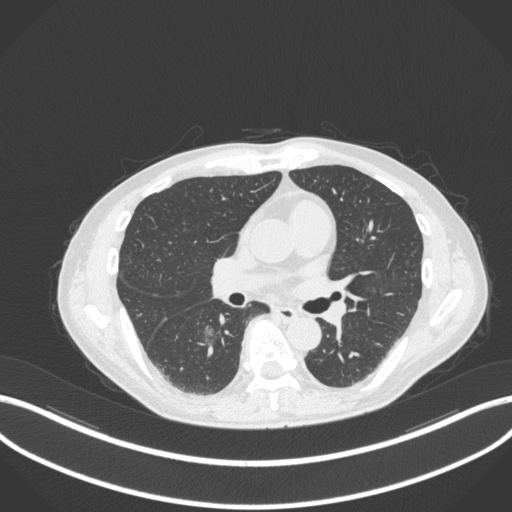
Chest CT, one axial slice. Slice 173 of 324 in the series (ordered by position). Reconstruction kernel B31f. 120 kVp. Lung window (W 1500 / L -600 HU). 1 mm slice thickness. 512 × 512 image matrix. Male patient, age 61 years. Case-level facts recorded for this patient, not image findings: clinical TNM (as recorded): T1c N0 M0.
Annotated regions visible in this slice (bounding box drawn by a radiologist):
- lung tumour (recorded histology: adenocarcinoma): bounding box <200,322,220,348> (left, top, right, bottom; pixels)